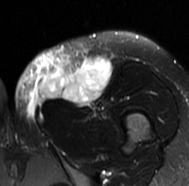
MRI of an extremity soft-tissue mass, one axial slice. Slice 30 of 77 in the series (ordered by position). T2-weighted fat-saturated. MR volume resampled by the dataset authors to the PET/CT grid (not the native acquisition matrix). 3.27 mm slice thickness. 189 × 186 image matrix. Female patient. Case-level facts recorded for this patient, not image findings: histological type: leiomyosarcoma; grade: high; site of the primary tumour: groin.
Structures marked on this image (expert contour drawn on MRI and transferred to this co-registered scan by the dataset authors):
- gross tumour volume including surrounding oedema: bounding box <13,47,112,121> (left, top, right, bottom; pixels)
- gross tumour volume (mass): <38,59,110,105>